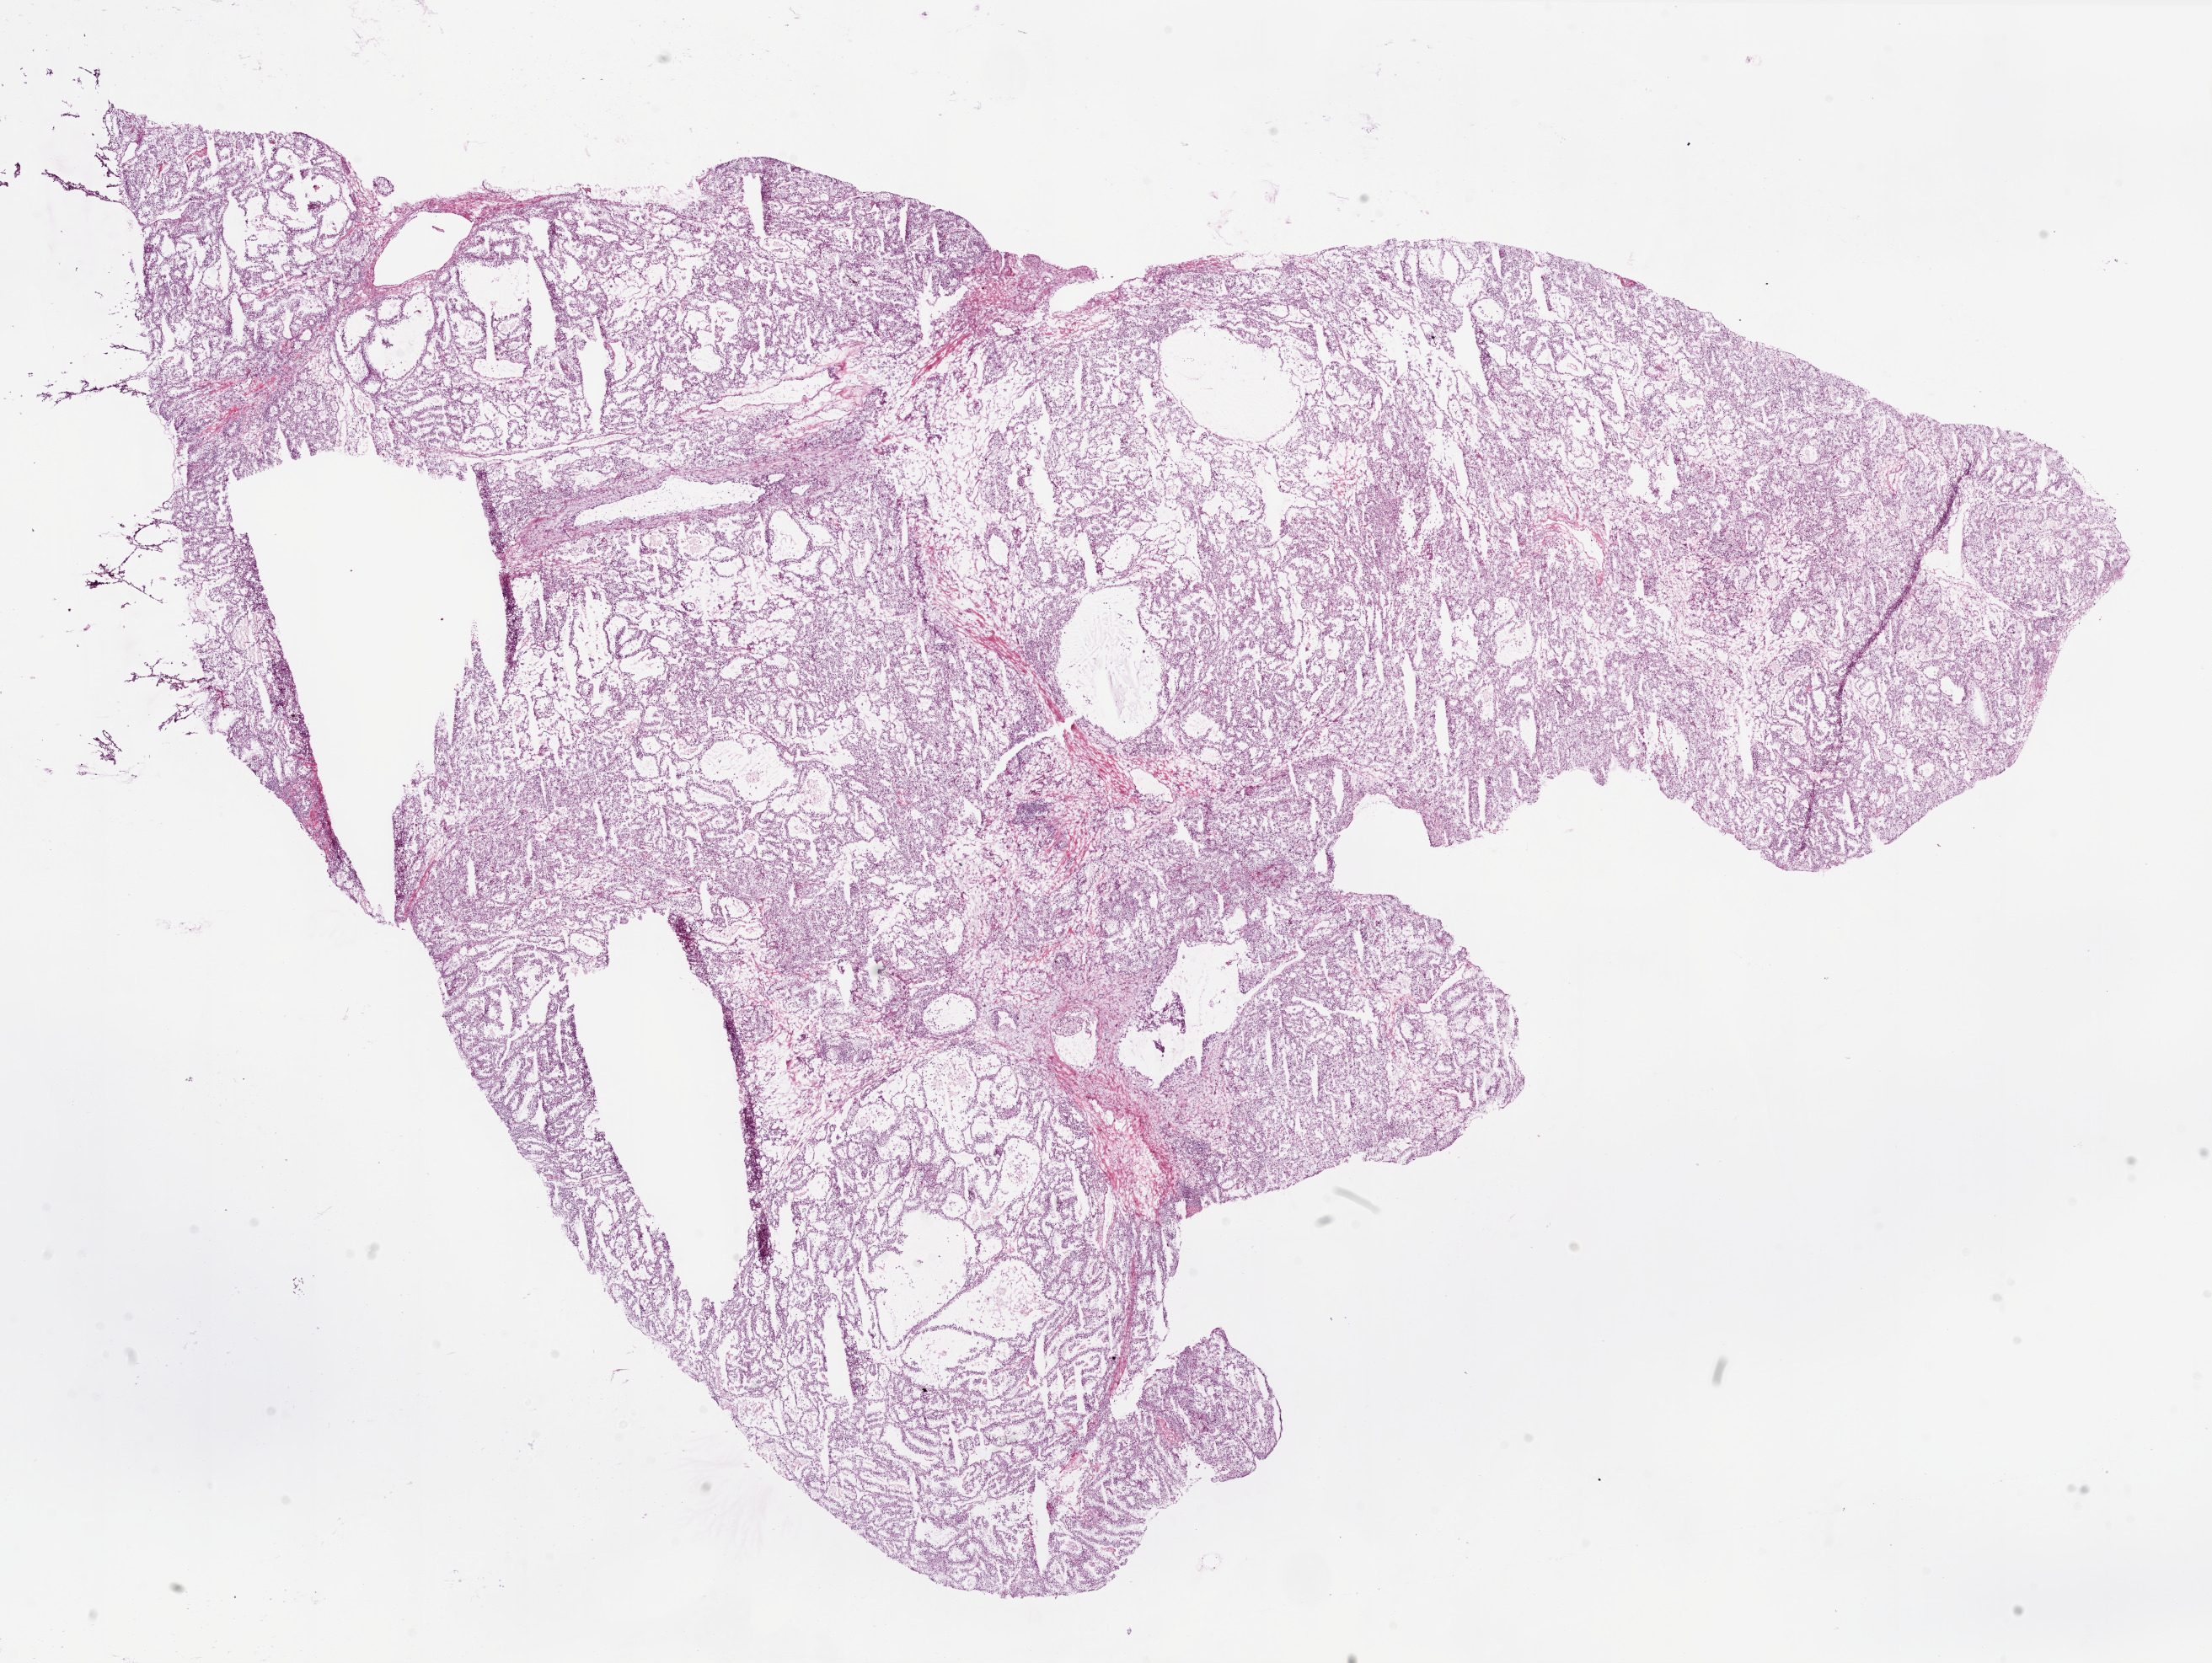
Digitized Hematoxylin and eosin (H&E) stained tissue section (whole slide), low-resolution overview of the scanned area, about 21.1 x 15.8 mm, frozen section, primary tumour sample from the kidney. Patient: female, age at initial diagnosis 70 years. Histologic grade: G2 (moderately differentiated). Pathologist review of this section (percent, as recorded): tumour cells 90%, tumour nuclei 80%, normal cells 0%, stromal cells 10%, necrosis 0%.
* AJCC pathologic stage: I
* diagnosis: Clear cell adenocarcinoma, NOS